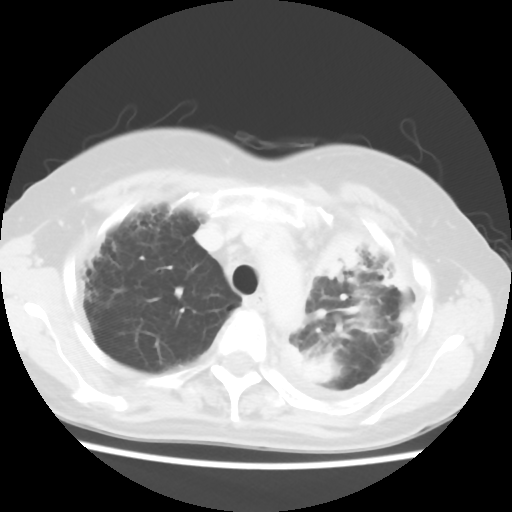
Chest CT, one axial slice. Position 43 of 56 along the scan axis. Reconstruction kernel STANDARD. 120 kVp. Lung window (W 1500 / L -600 HU). 5 mm slice thickness. 512 × 512 image matrix, field of view 309 × 309 mm. Patient: female, 56 years. Case-level facts recorded for this patient, not image findings: clinical TNM (as recorded): T1c N0 M1.
Annotated regions visible in this slice (rectangle marked by the reading radiologist):
- lung tumour (recorded histology: adenocarcinoma): bounding box <321,221,362,292> (left, top, right, bottom; pixels)